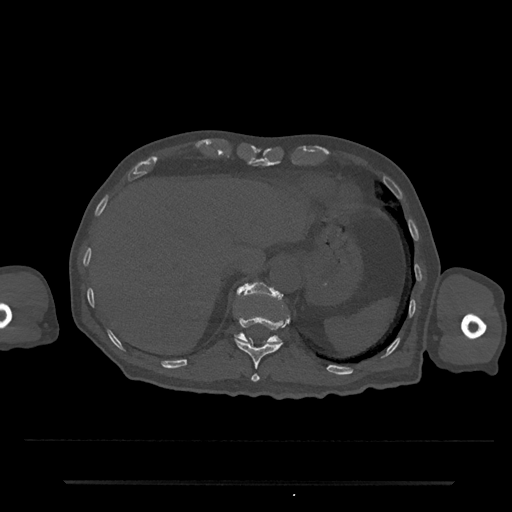
CT including the spine, one axial slice; position 239 of 797 along the scan axis; reconstruction kernel Br40s/3; bone window (W 1800 / L 400 HU); 0.5 mm slice thickness; 512 × 512 image matrix. Patient: male, 74 years. Case-level facts recorded for this patient, not image findings: primary cancer: prostate.
Outlined on this slice (semi-automatically segmented with operator editing):
- T11 vertebra: bounding box <235,316,289,382> (left, top, right, bottom; pixels)
- T12 vertebra: <235,282,281,344>